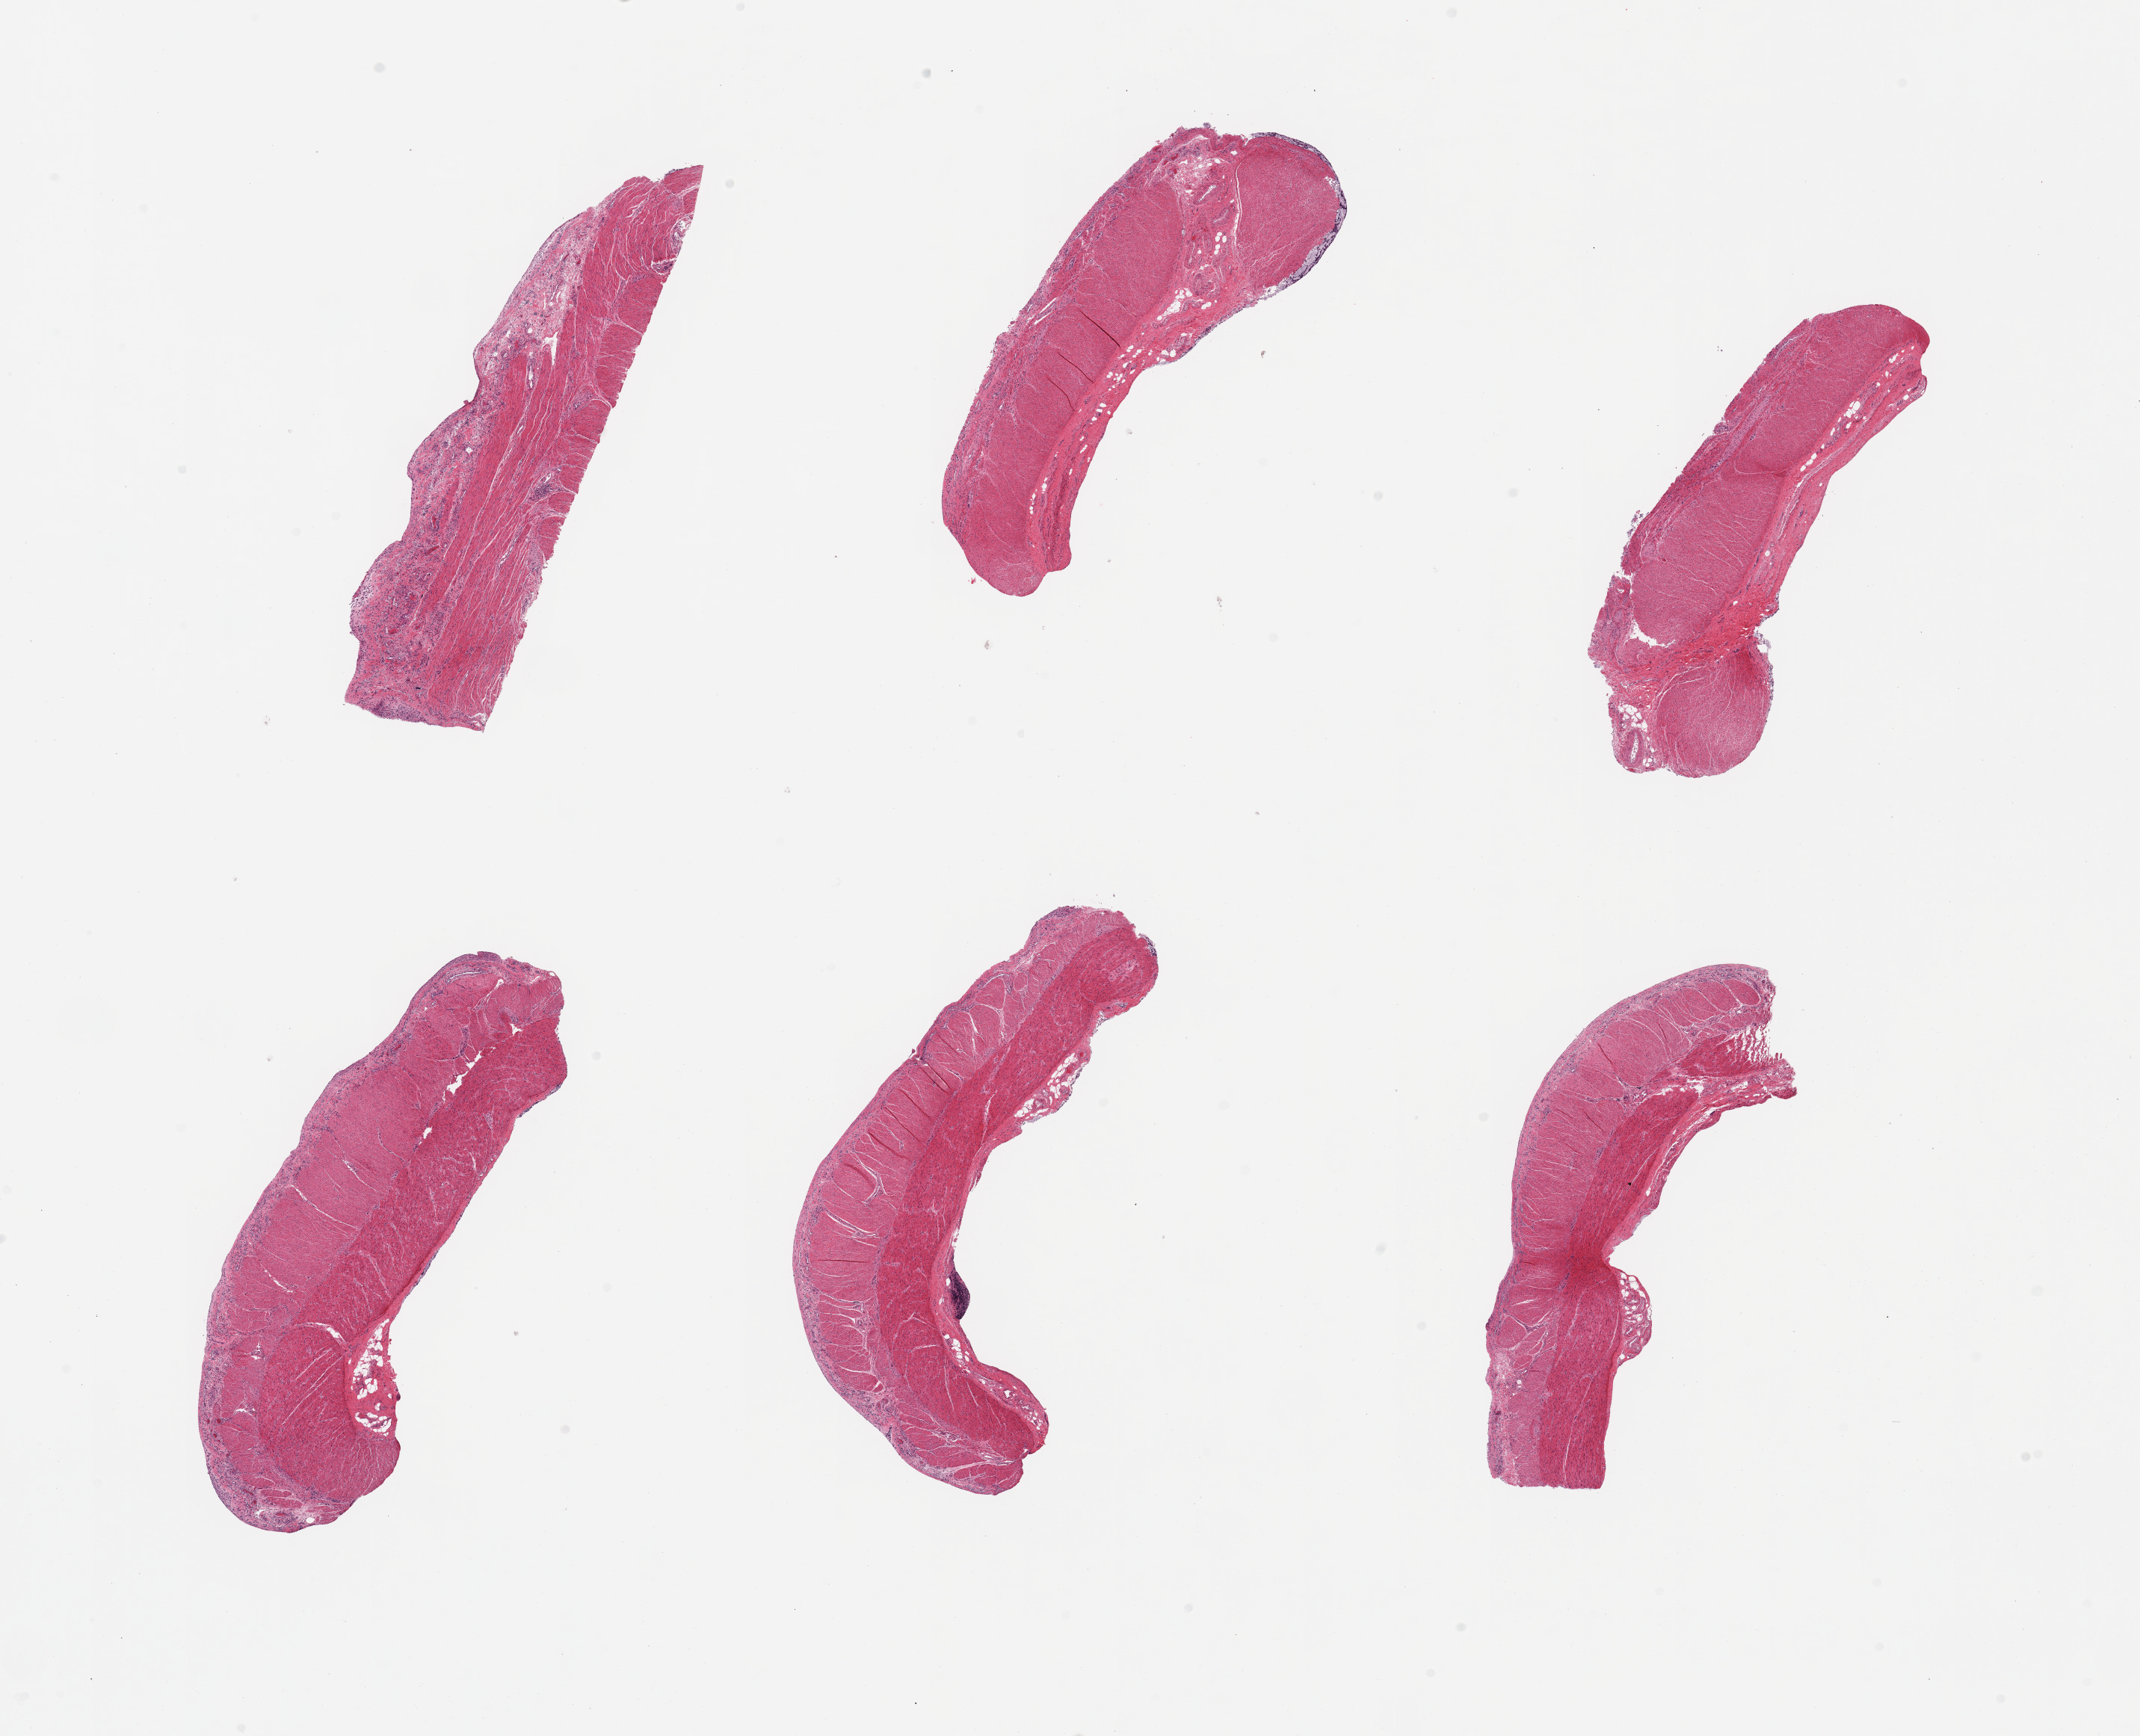
Haematoxylin and eosin whole-slide image, brightfield, whole scanned area (about 22.6 x 18.4 mm) shown as a low-resolution overview, PAXgene-fixed, paraffin-embedded tissue, sampled site (target tissue): sigmoid colon, donor tissue sample. Donor: male.
* reviewer comment on this tissue sample: 6 pieces; muscularis, serositis